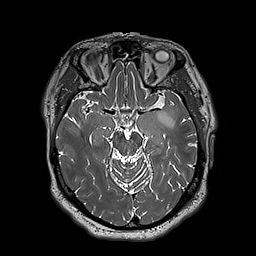
Brain MRI from a brain-tumour surgery series, one axial slice; position 120 of 192 along the scan axis; 256 × 256 image matrix. Case-level facts recorded for this patient, not image findings: histopathology: Astrocytoma; WHO grade: 3; IDH mutation: yes; tumour location: Left Insular.
Annotated regions visible in this slice (expert manual segmentation):
- tumour: bounding box [x1, y1, x2, y2] px = [154, 106, 174, 127]